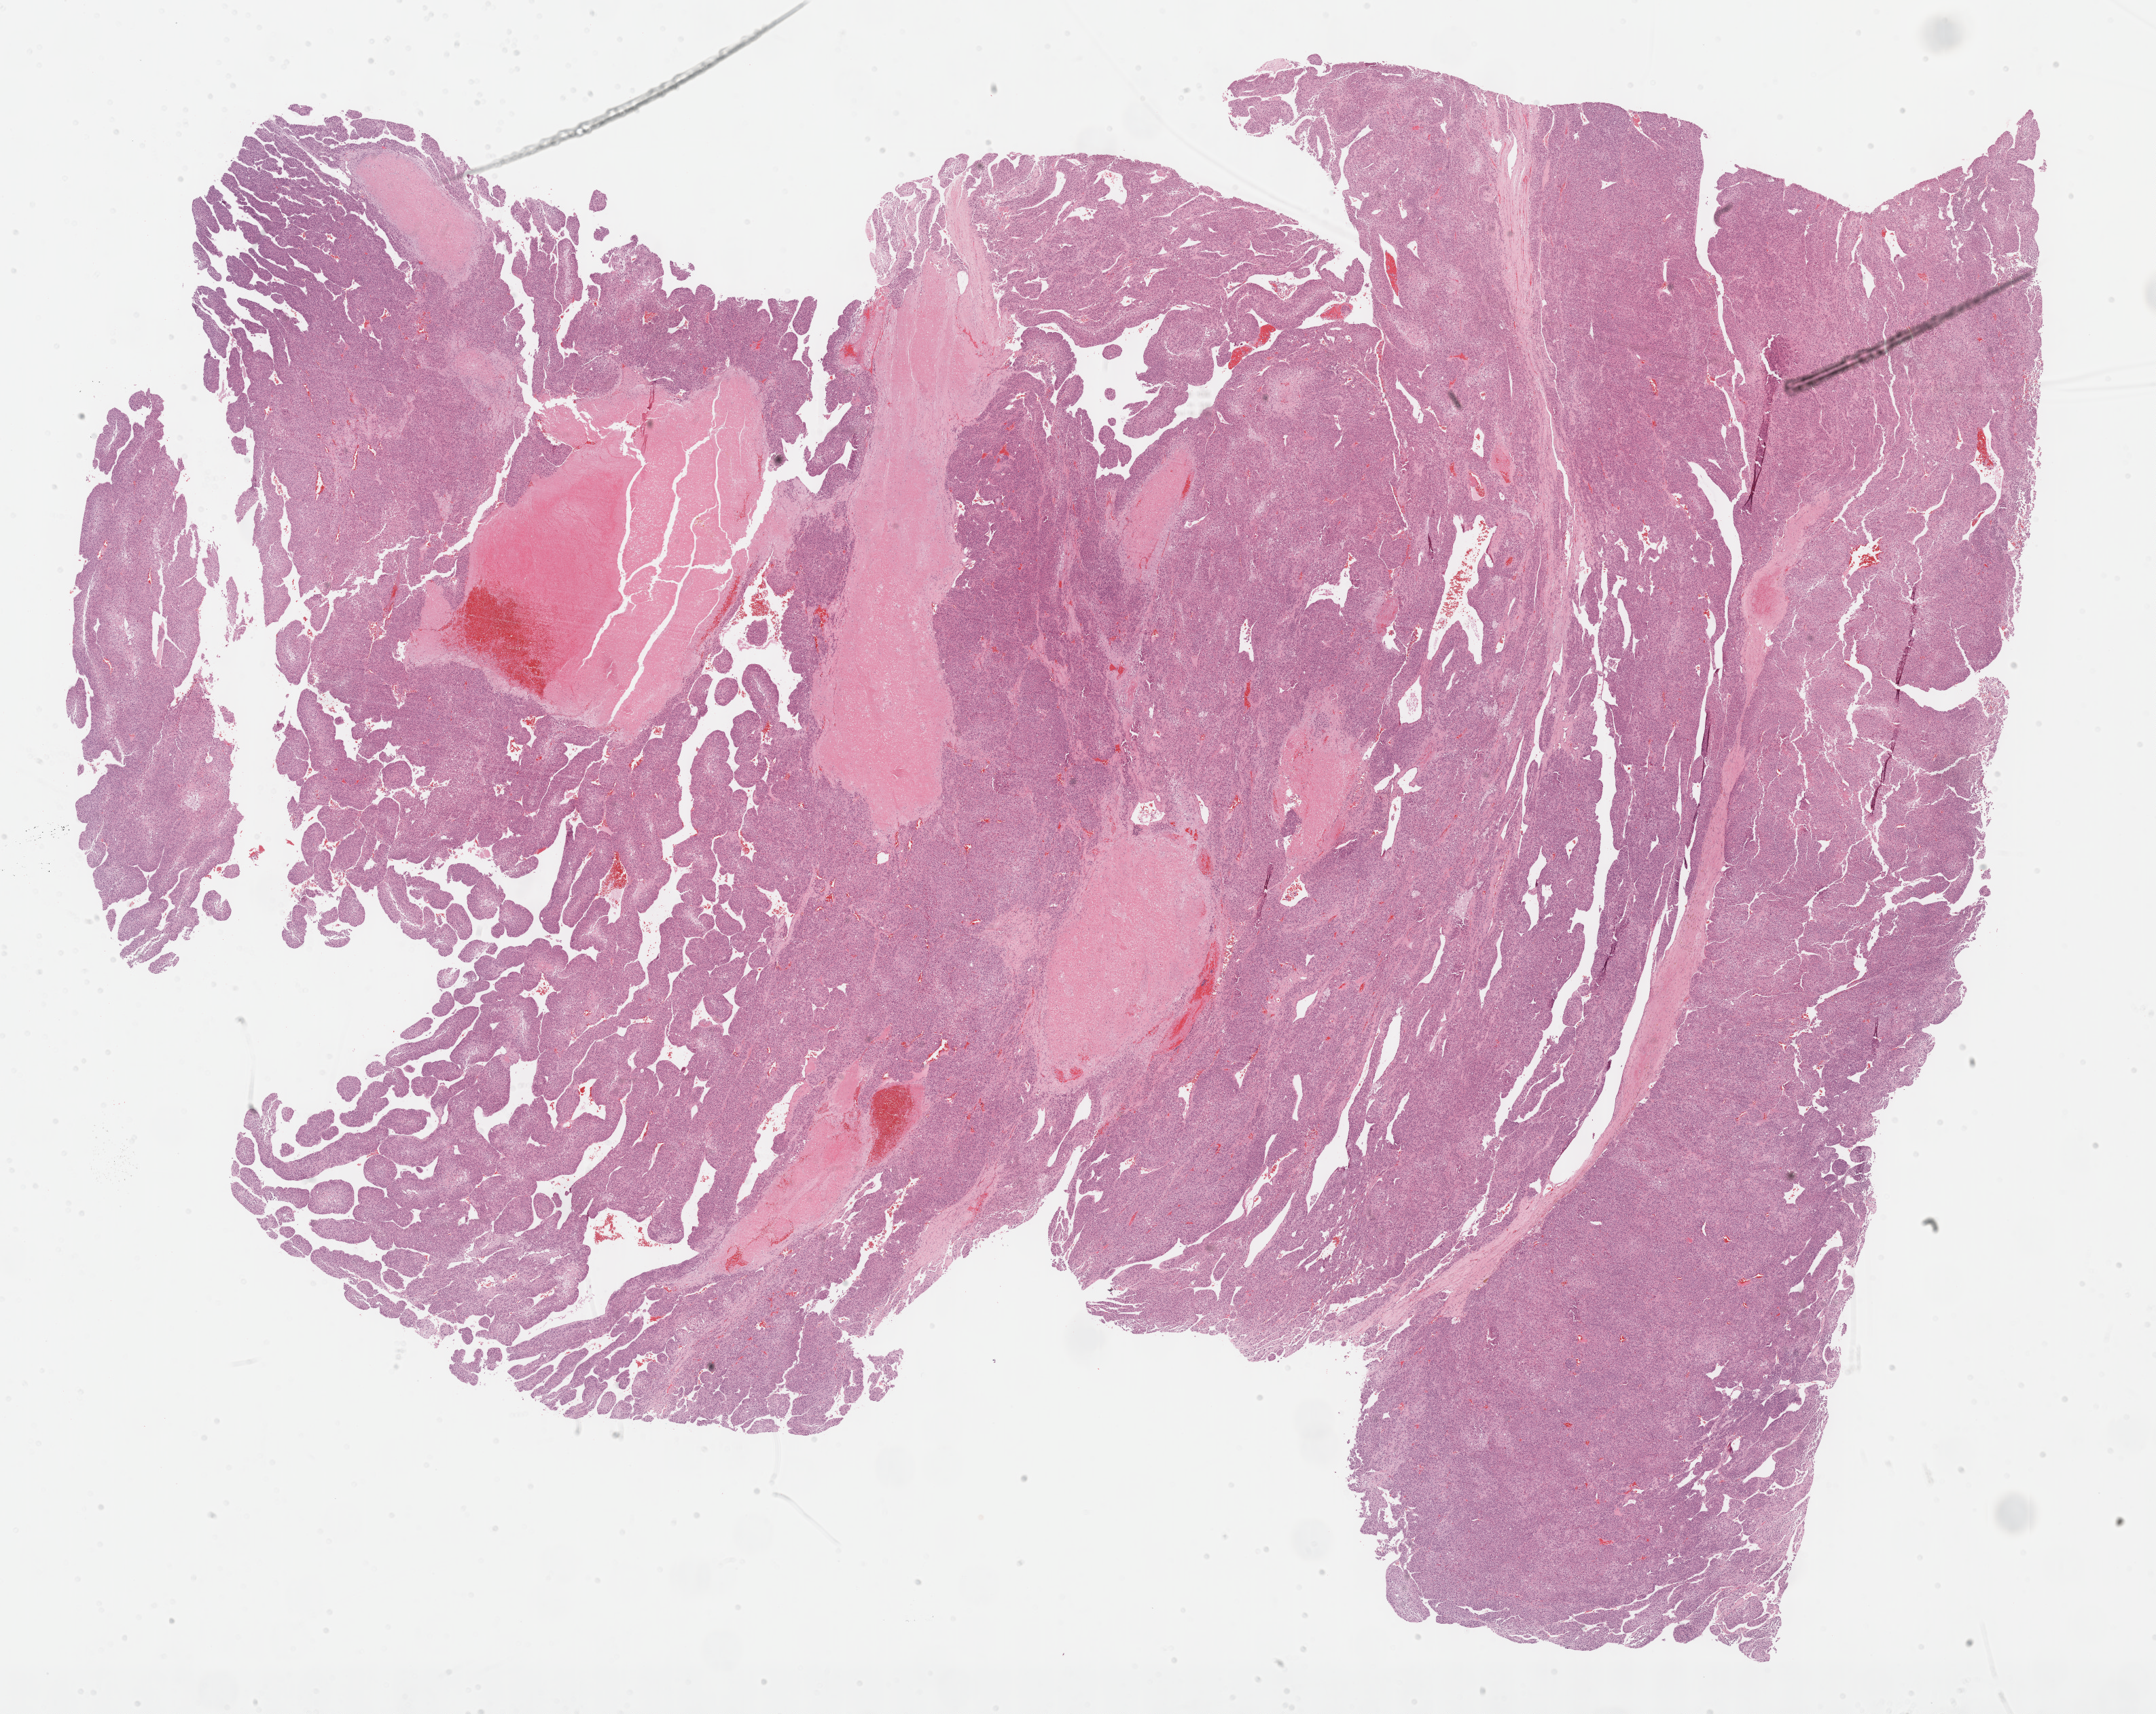
Digitized Hematoxylin and eosin (H&E) stained tissue section (whole slide) — shown as a low-resolution overview of the whole scanned area (about 25.7 x 20.4 mm, slide scanned at 40x). Formalin-fixed paraffin-embedded (FFPE) diagnostic section. Sample: primary tumour, adrenal cortex. Patient: female, age at initial diagnosis 59 years.
Diagnosis: Adrenal cortical carcinoma (cortex of adrenal gland). Lymph nodes positive (case pathology): 0 of 20 examined.